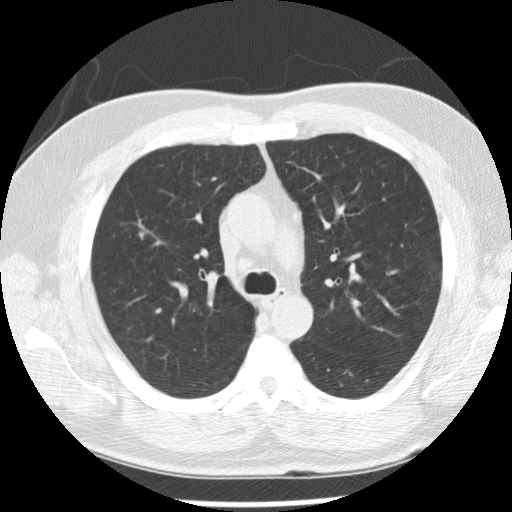
Low-dose screening chest CT, axial slice. Baseline screening round. Lung window (W 1500 / L -600 HU). 2.5 mm slice thickness. Standard (soft-tissue) reconstruction kernel (STANDARD). 120 kVp. 512 × 512 image matrix, field of view 340 × 340 mm. Male, age 57 years at enrolment.
Expert-annotated lung lesion, box from (x=126, y=222) to (x=159, y=253) px. The exam's reader record, not a measurement of the box and not confirmed to be the same lesion: non-calcified nodule or mass ≥4 mm, right upper lobe, 7 × 7 mm, poorly defined margins, soft tissue attenuation. Participant outcome: lung cancer diagnosed 125 days after this screen — squamous cell carcinoma, NOS, right upper lobe, moderately differentiated (G2), stage IA (AJCC 6th edition), 10 mm at pathology.